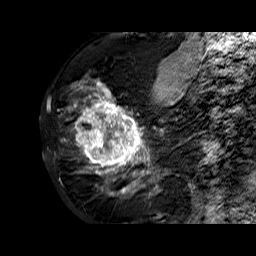
Breast MRI (dynamic contrast-enhanced), one sagittal slice; slice 26 of 60 in the series (ordered by position); dynamic contrast-enhanced series, time point 2 of 6 at this slice position (early post-contrast); 1.5 T; TE 6.3 ms, TR 32.4 ms; 256 × 256 image matrix, field of view 200 × 200 mm. Female patient. Case-level facts recorded for this patient, not image findings: setting: breast cancer imaged before/during neoadjuvant chemotherapy; receptor status: HR-positive, HER2-negative.
Outlined on this slice (semi-automatic segmentation, software-assisted and operator-edited):
- analysis volume of interest (the breast-tissue region the enhancement analysis was run in; not a lesion): bounding box <68,72,177,183> (left, top, right, bottom; pixels)
- tumour enhancement mask (voxels above the 100 % enhancement threshold inside the analysis volume of interest): <76,84,162,177>